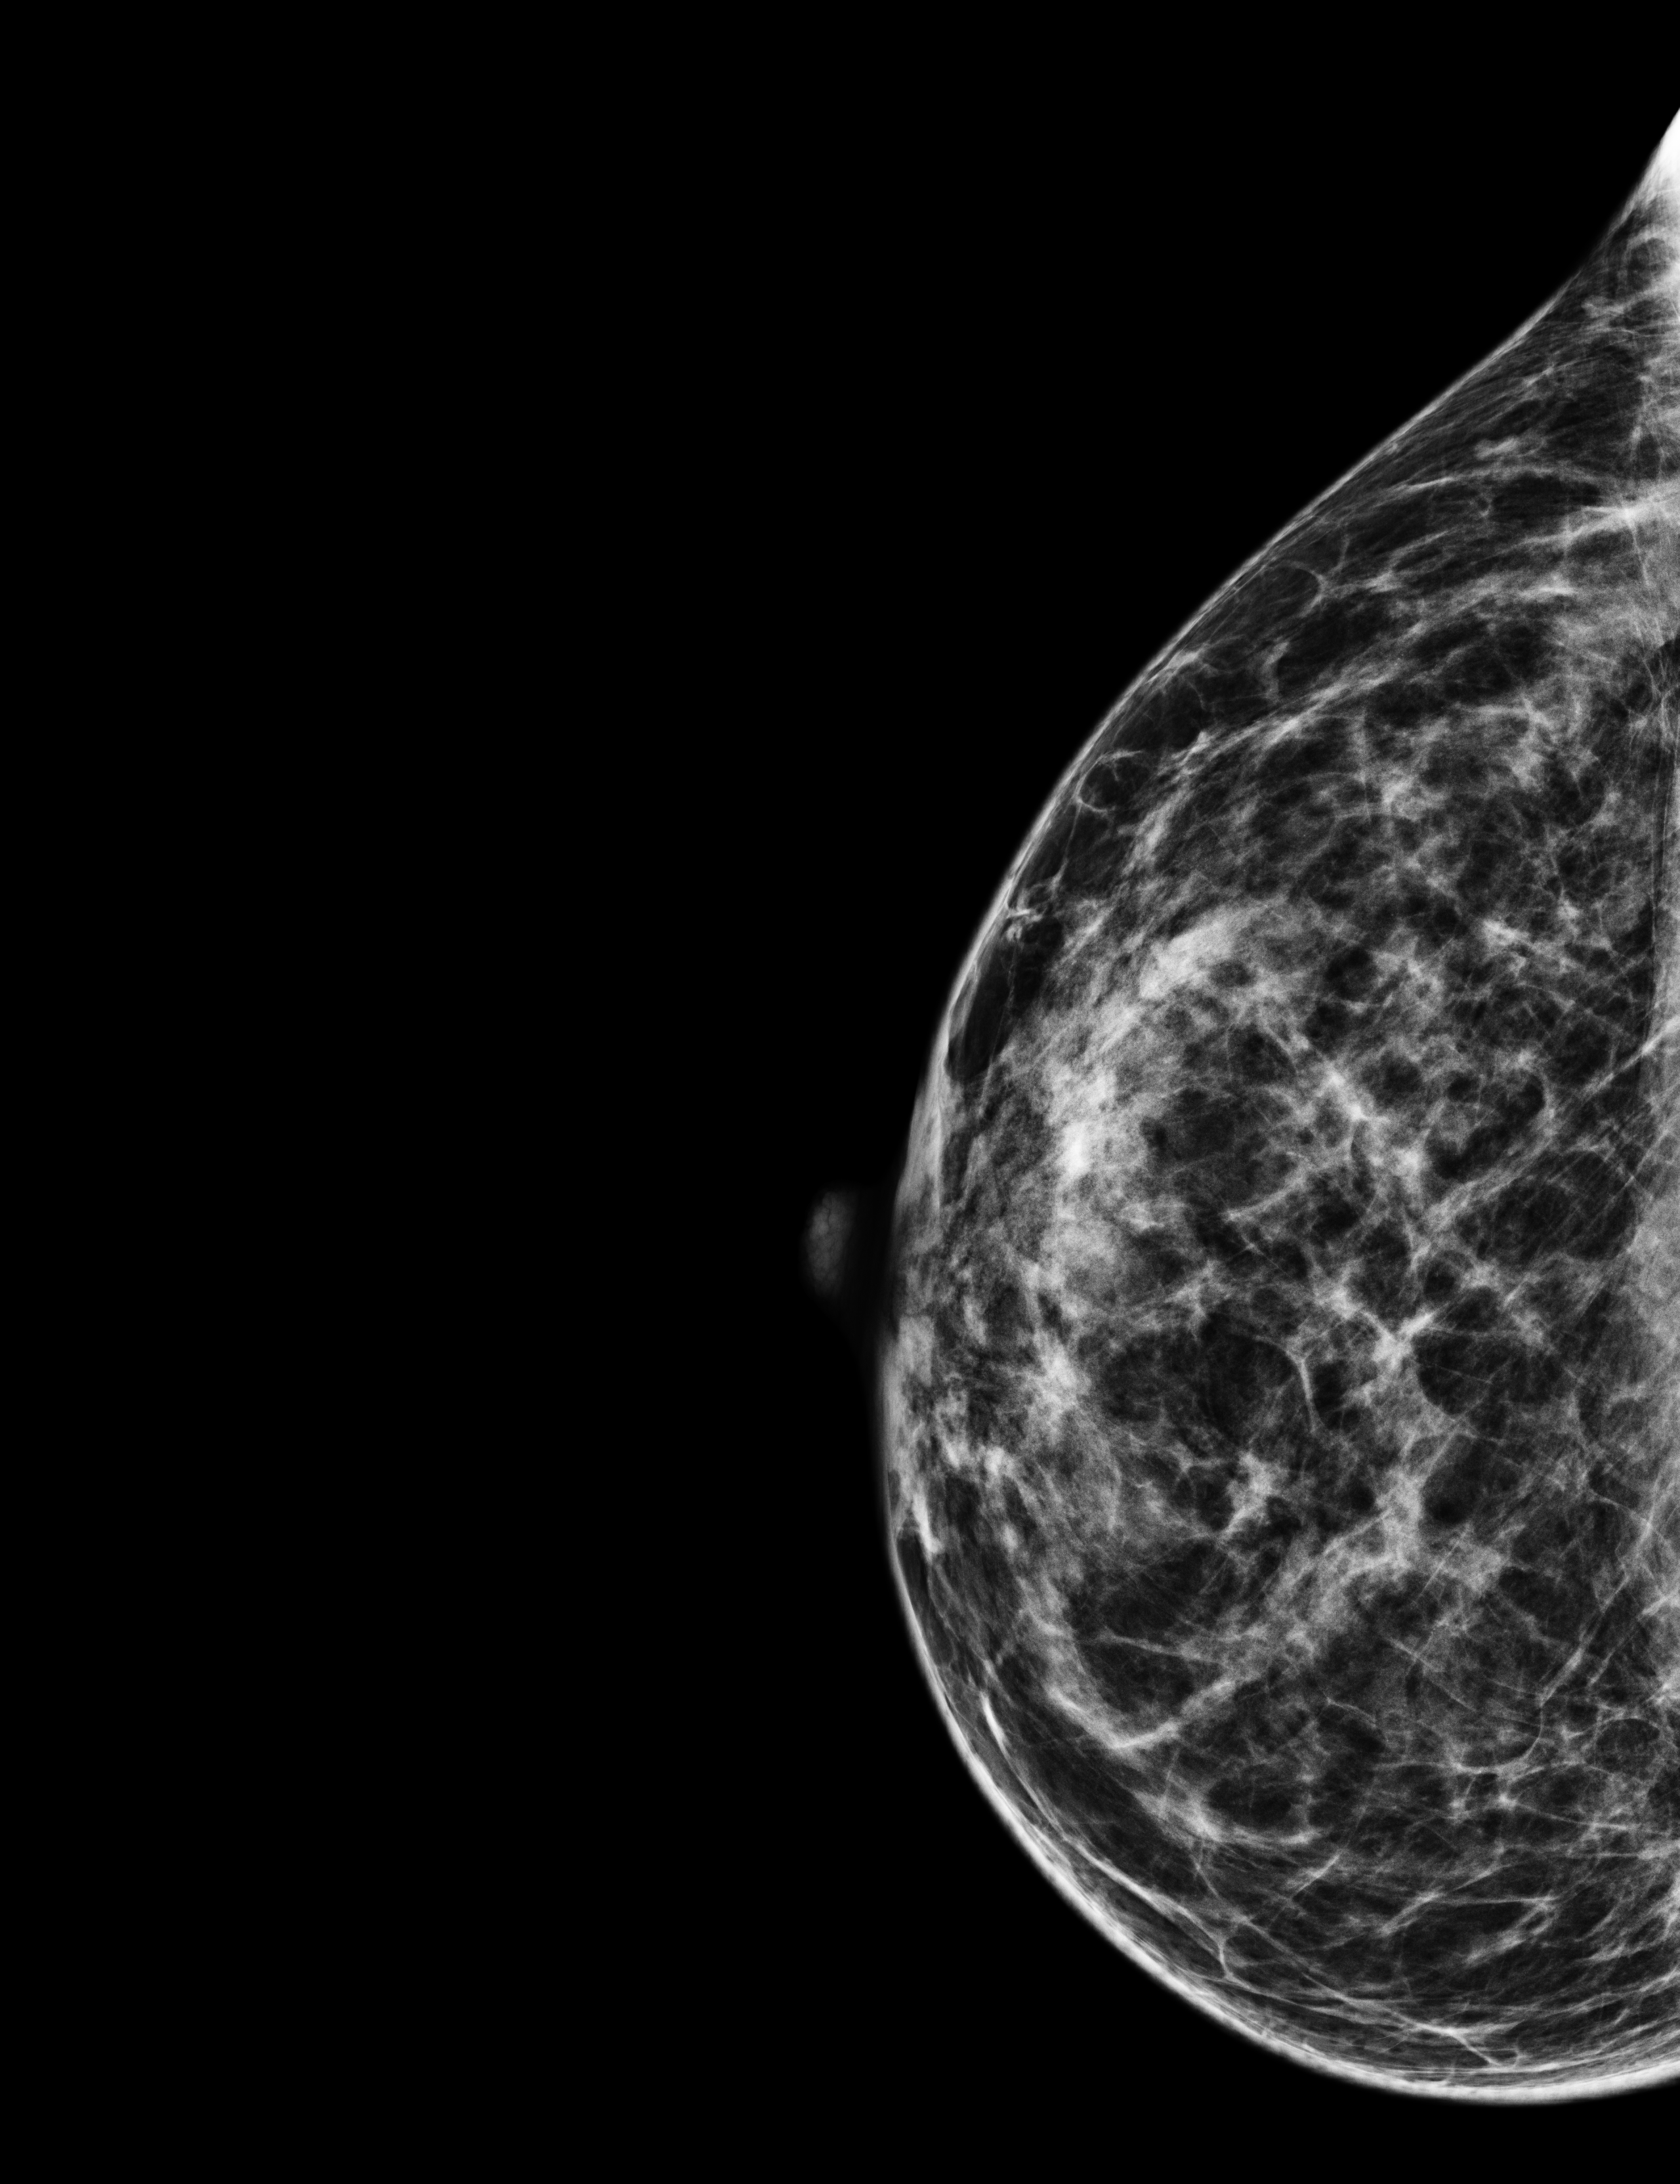
Annual screening mammography examination, compressed breast thickness 62 mm, system: Selenia Dimensions. Patient: female, 44 years.
Image type: full-field digital mammogram. Breast: right. Projection: craniocaudal (CC) view.